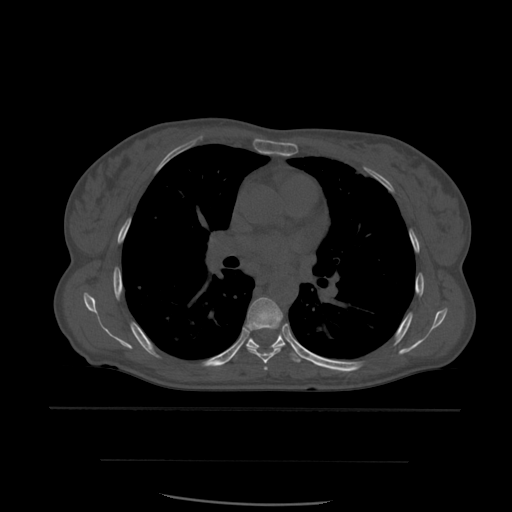
CT including the spine, one axial slice. Bone window (W 1800 / L 400 HU). 1.25 mm slice thickness. 512 × 512 image matrix, field of view 392 × 392 mm. Patient age 48 years. Case-level facts recorded for this patient, not image findings: primary cancer: lung; vertebrae with lytic lesions (as recorded): T11.
Outlined on this slice (semi-automatically segmented with operator editing):
- T5 vertebra: box from (x=264, y=367) to (x=268, y=371) px
- T6 vertebra: (x=246, y=297)–(x=286, y=364)
- T7 vertebra: (x=228, y=329)–(x=303, y=363)